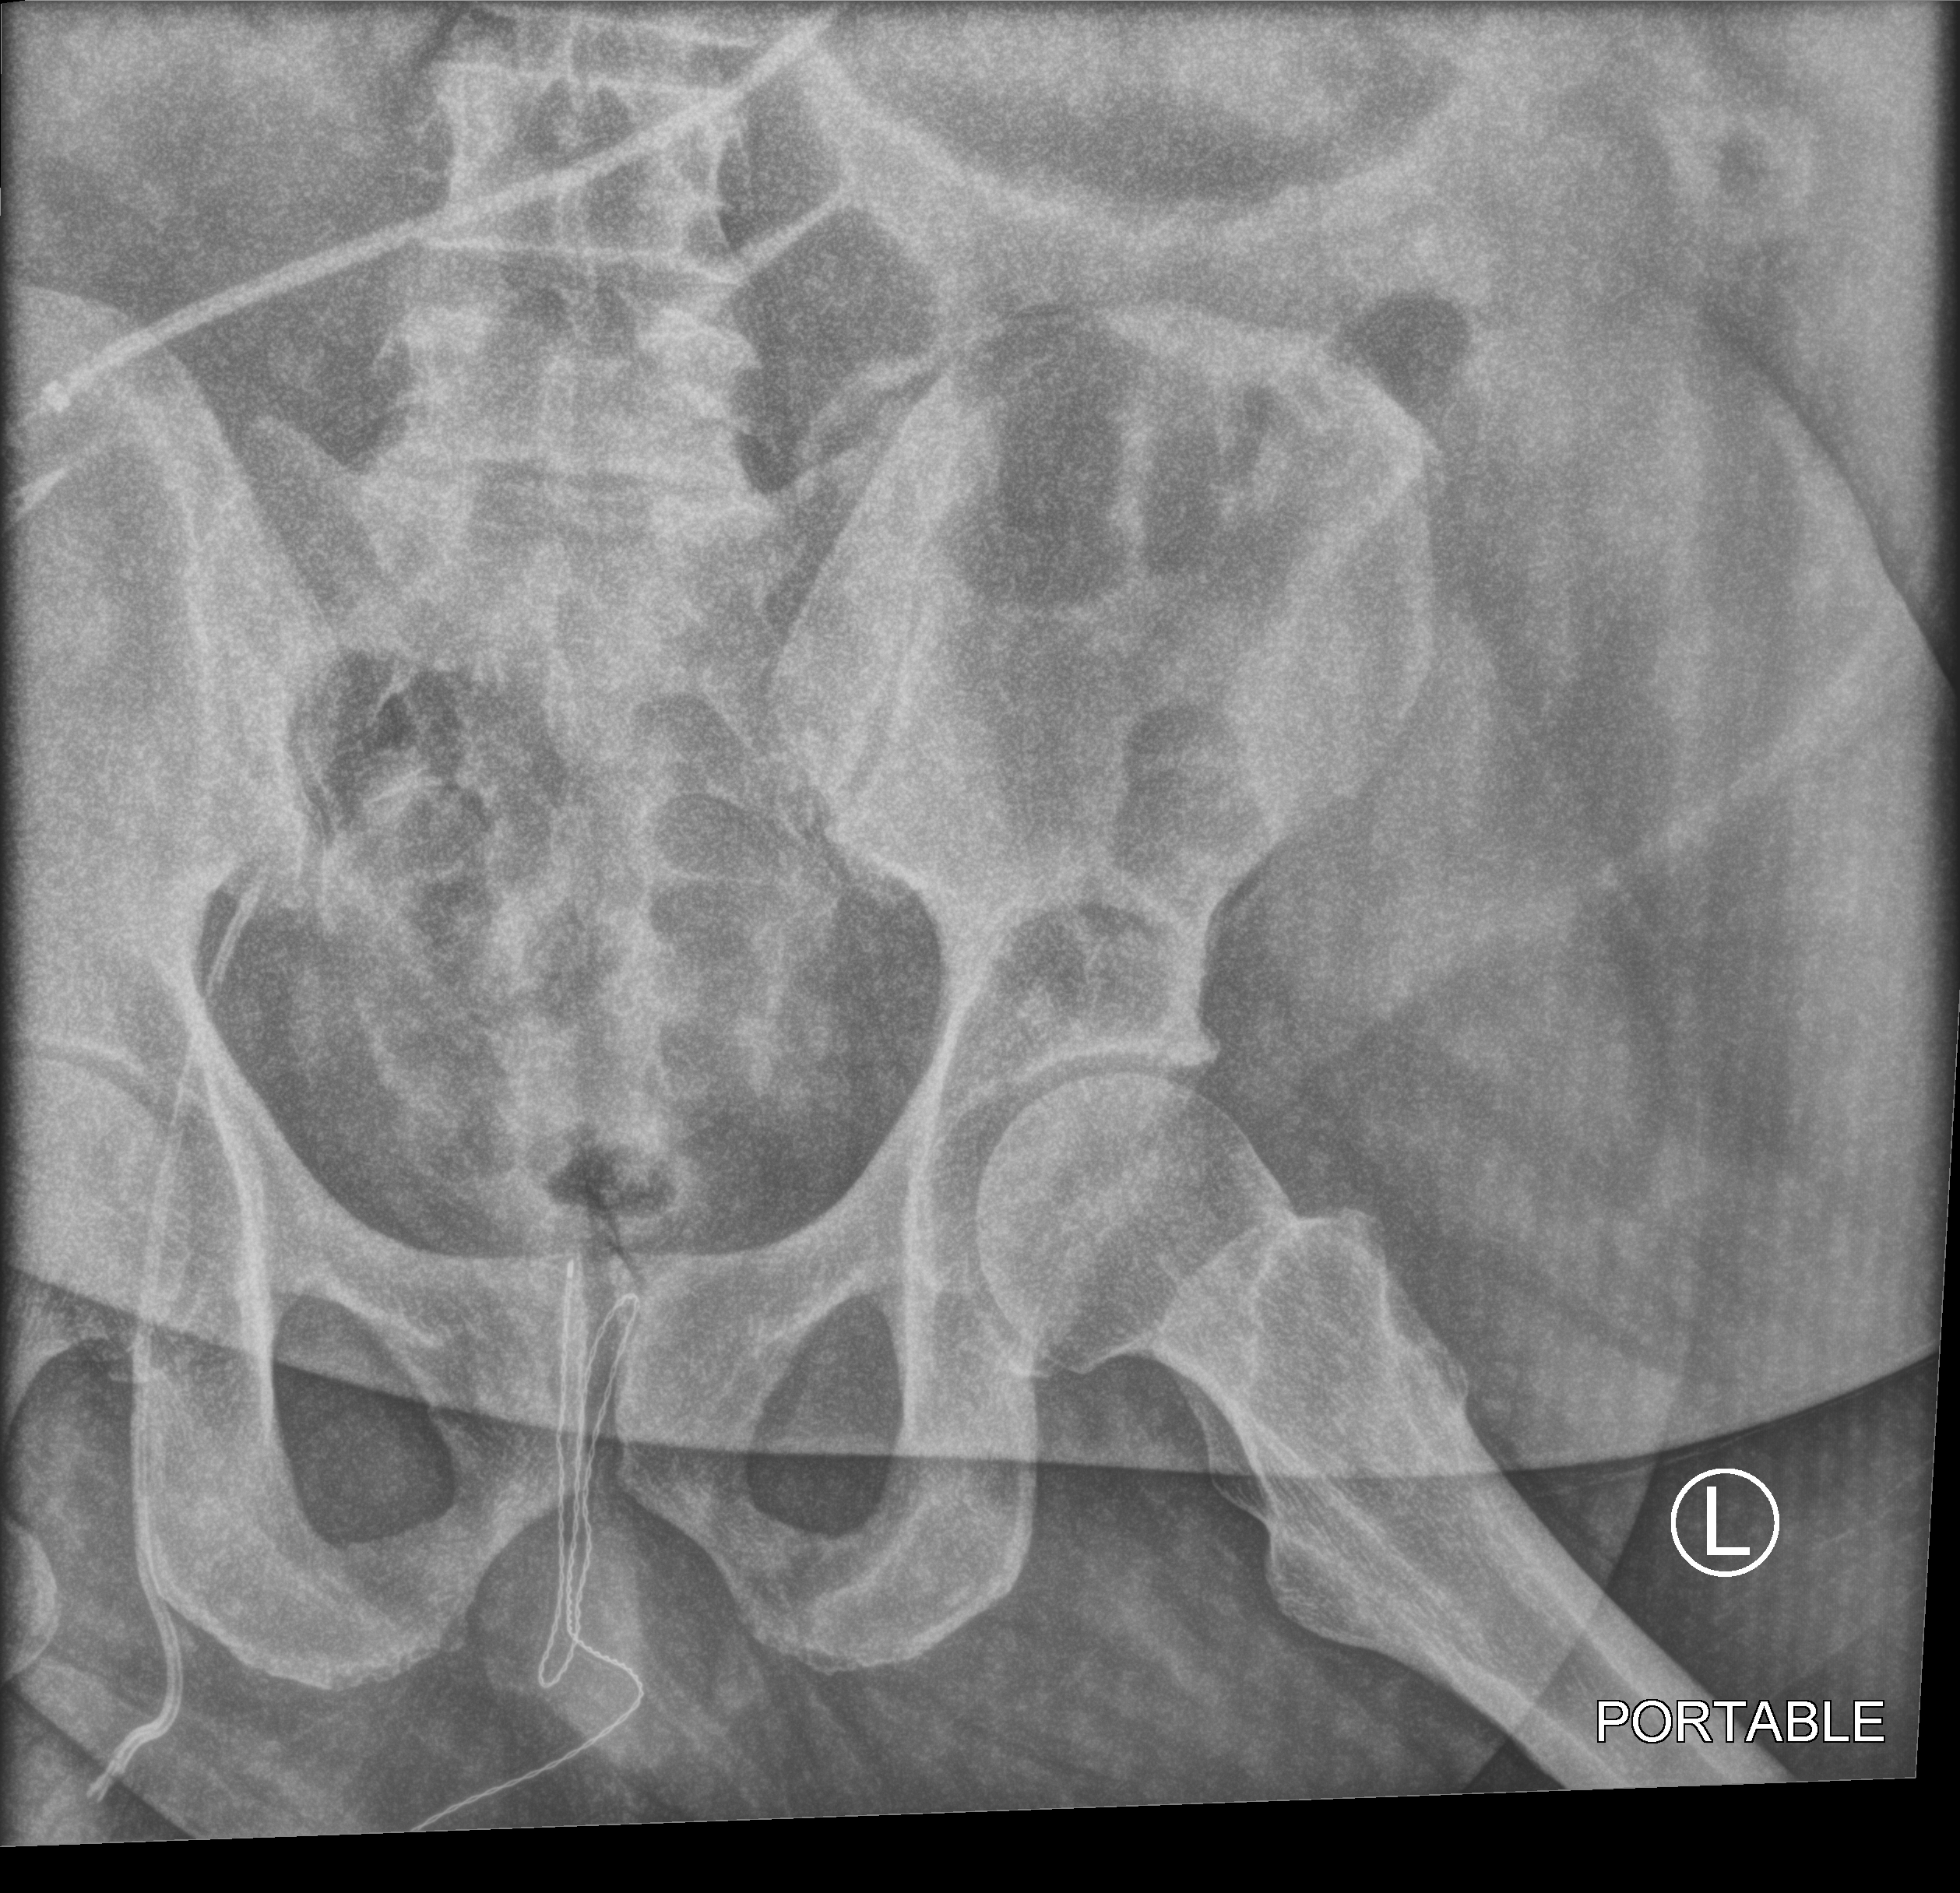
Bedside abdomen radiograph (computed radiography). Male patient hospitalised with COVID-19, age 60–74 years.
Hospital-stay facts (about this admission, not read from this image; timing relative to this image not recorded):
- smoking status (admission record): former